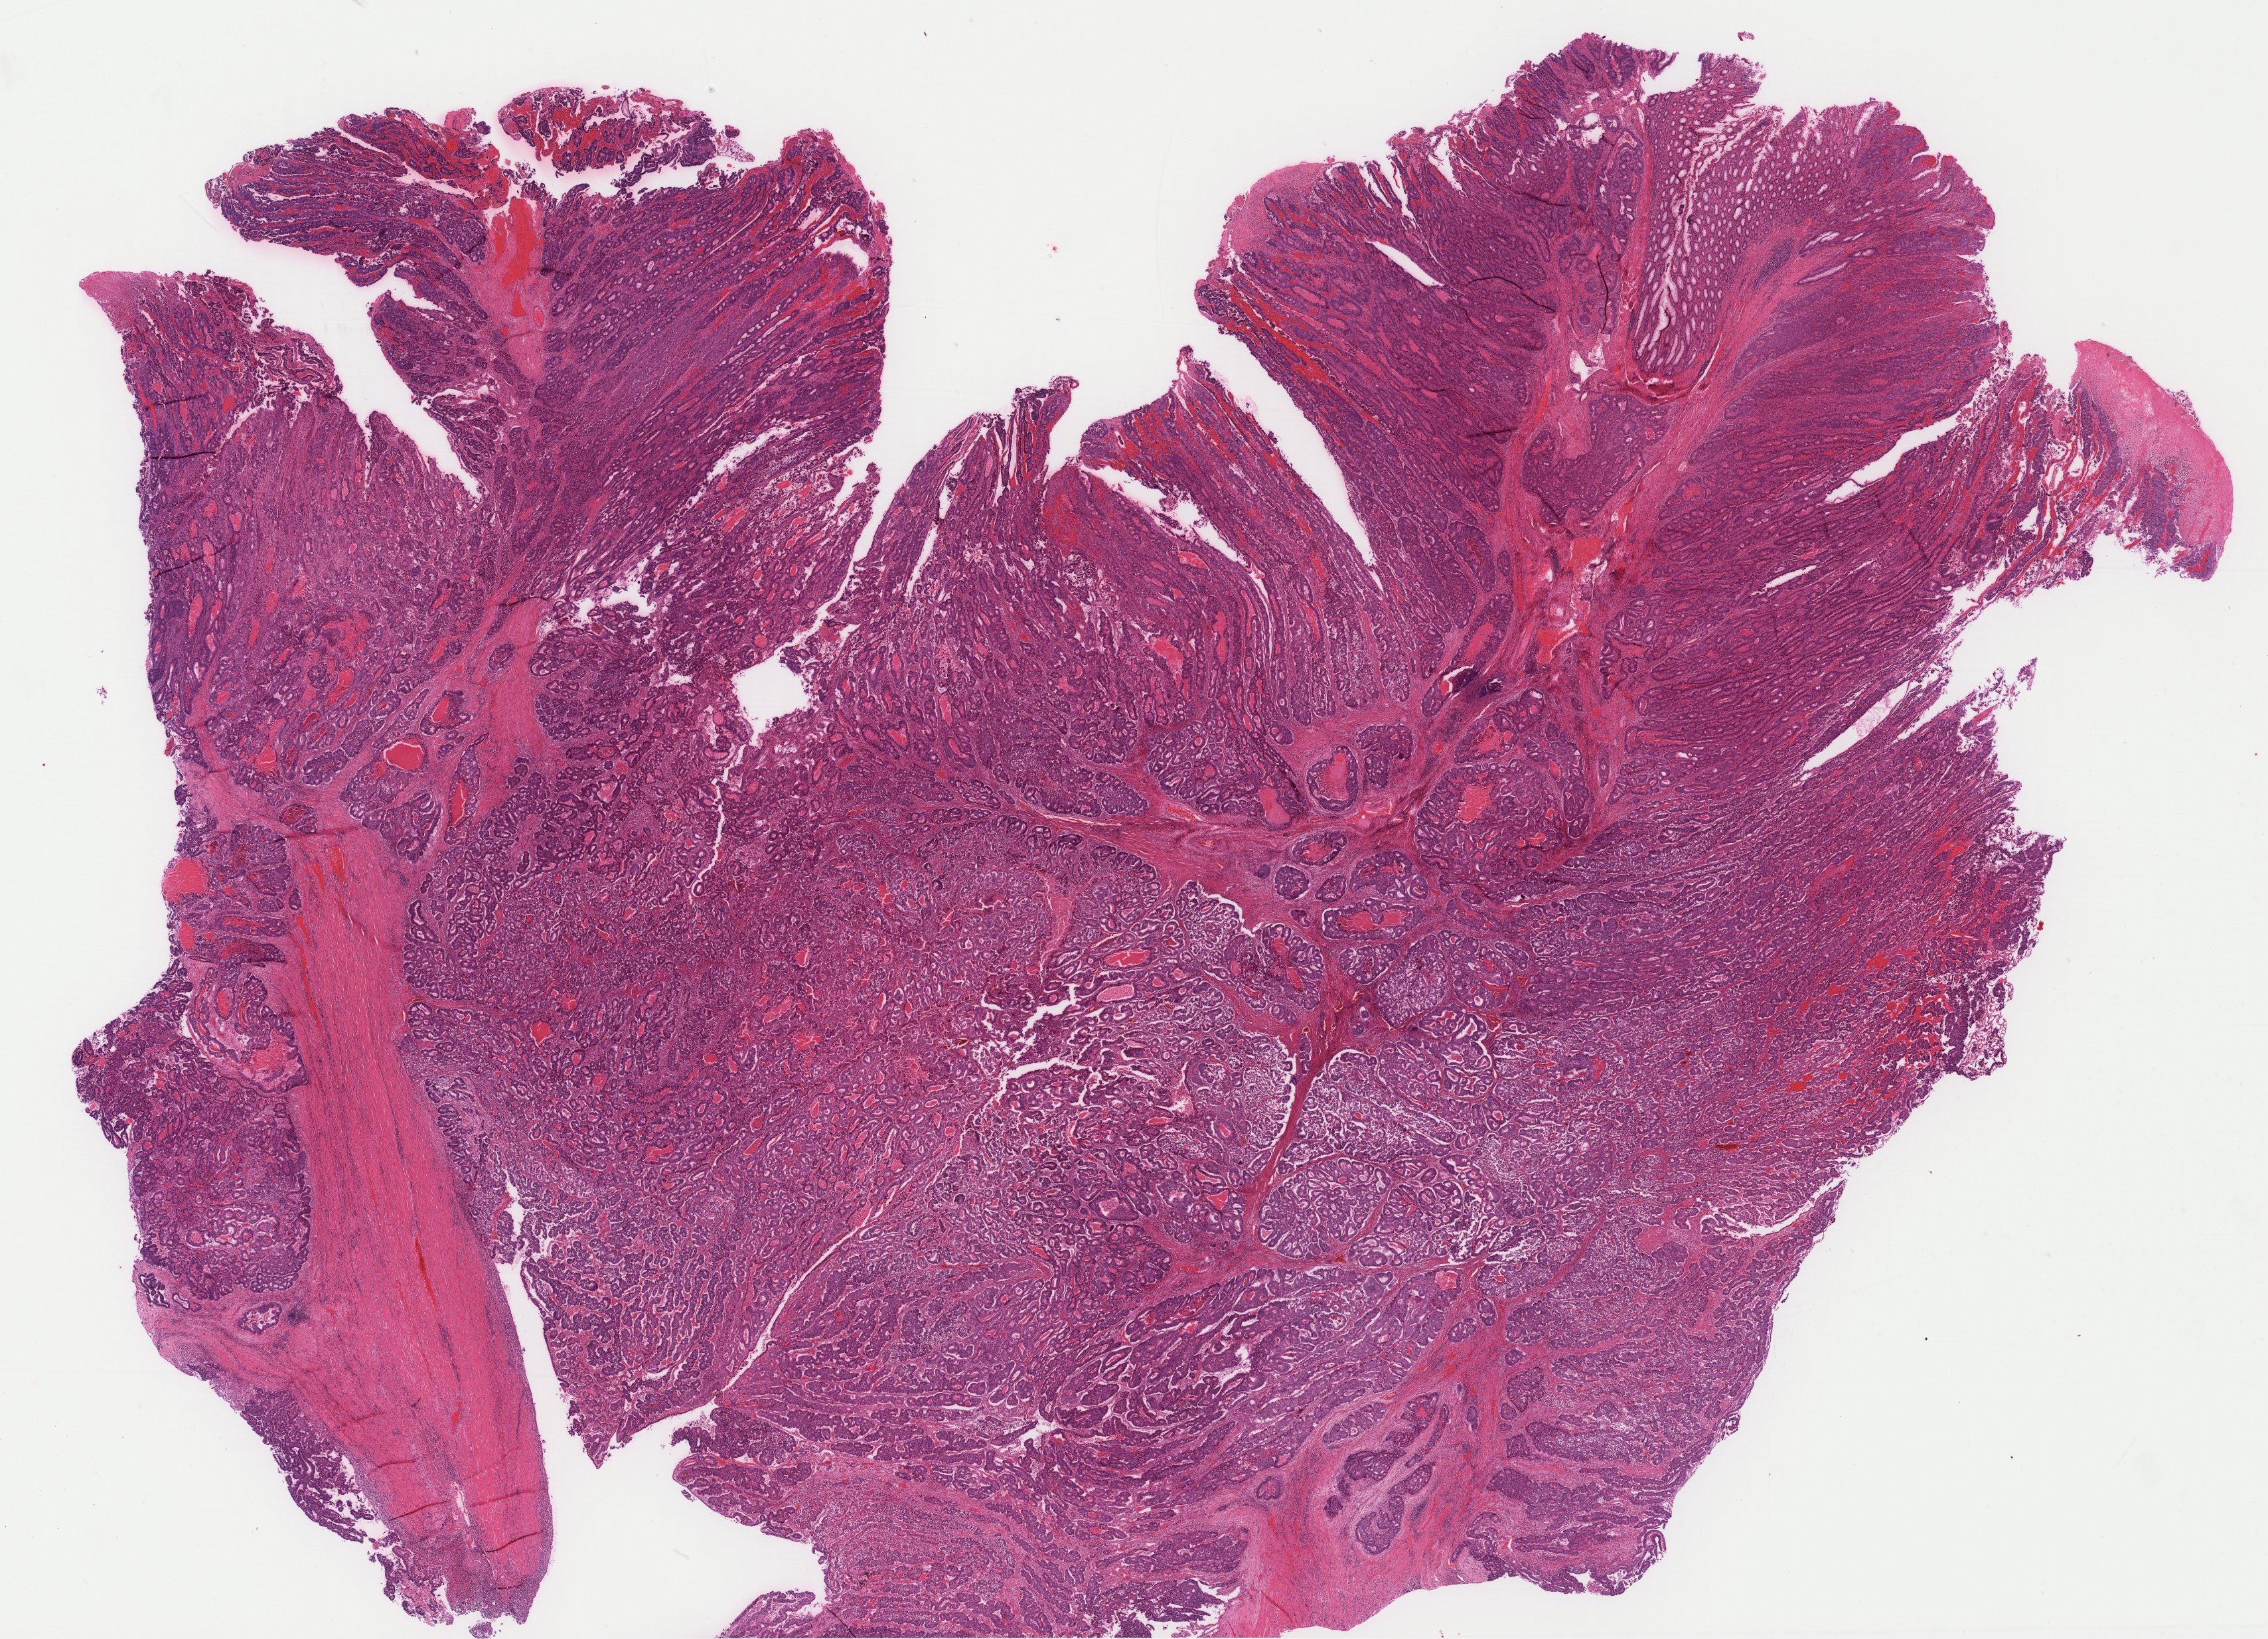
H&E whole-slide image — low-resolution overview of the scanned area, about 27.7 x 20.0 mm (acquisition: 40x scan); formalin-fixed paraffin-embedded (FFPE) diagnostic section; colon, primary tumour sample. Female, age 44 years at initial diagnosis.
• TNM: T4a N0 M0
• lymph nodes positive (case pathology): 0 of 25 examined
• histologic diagnosis: Adenocarcinoma, NOS (cecum)
• AJCC pathologic stage: IIB (7th edition)